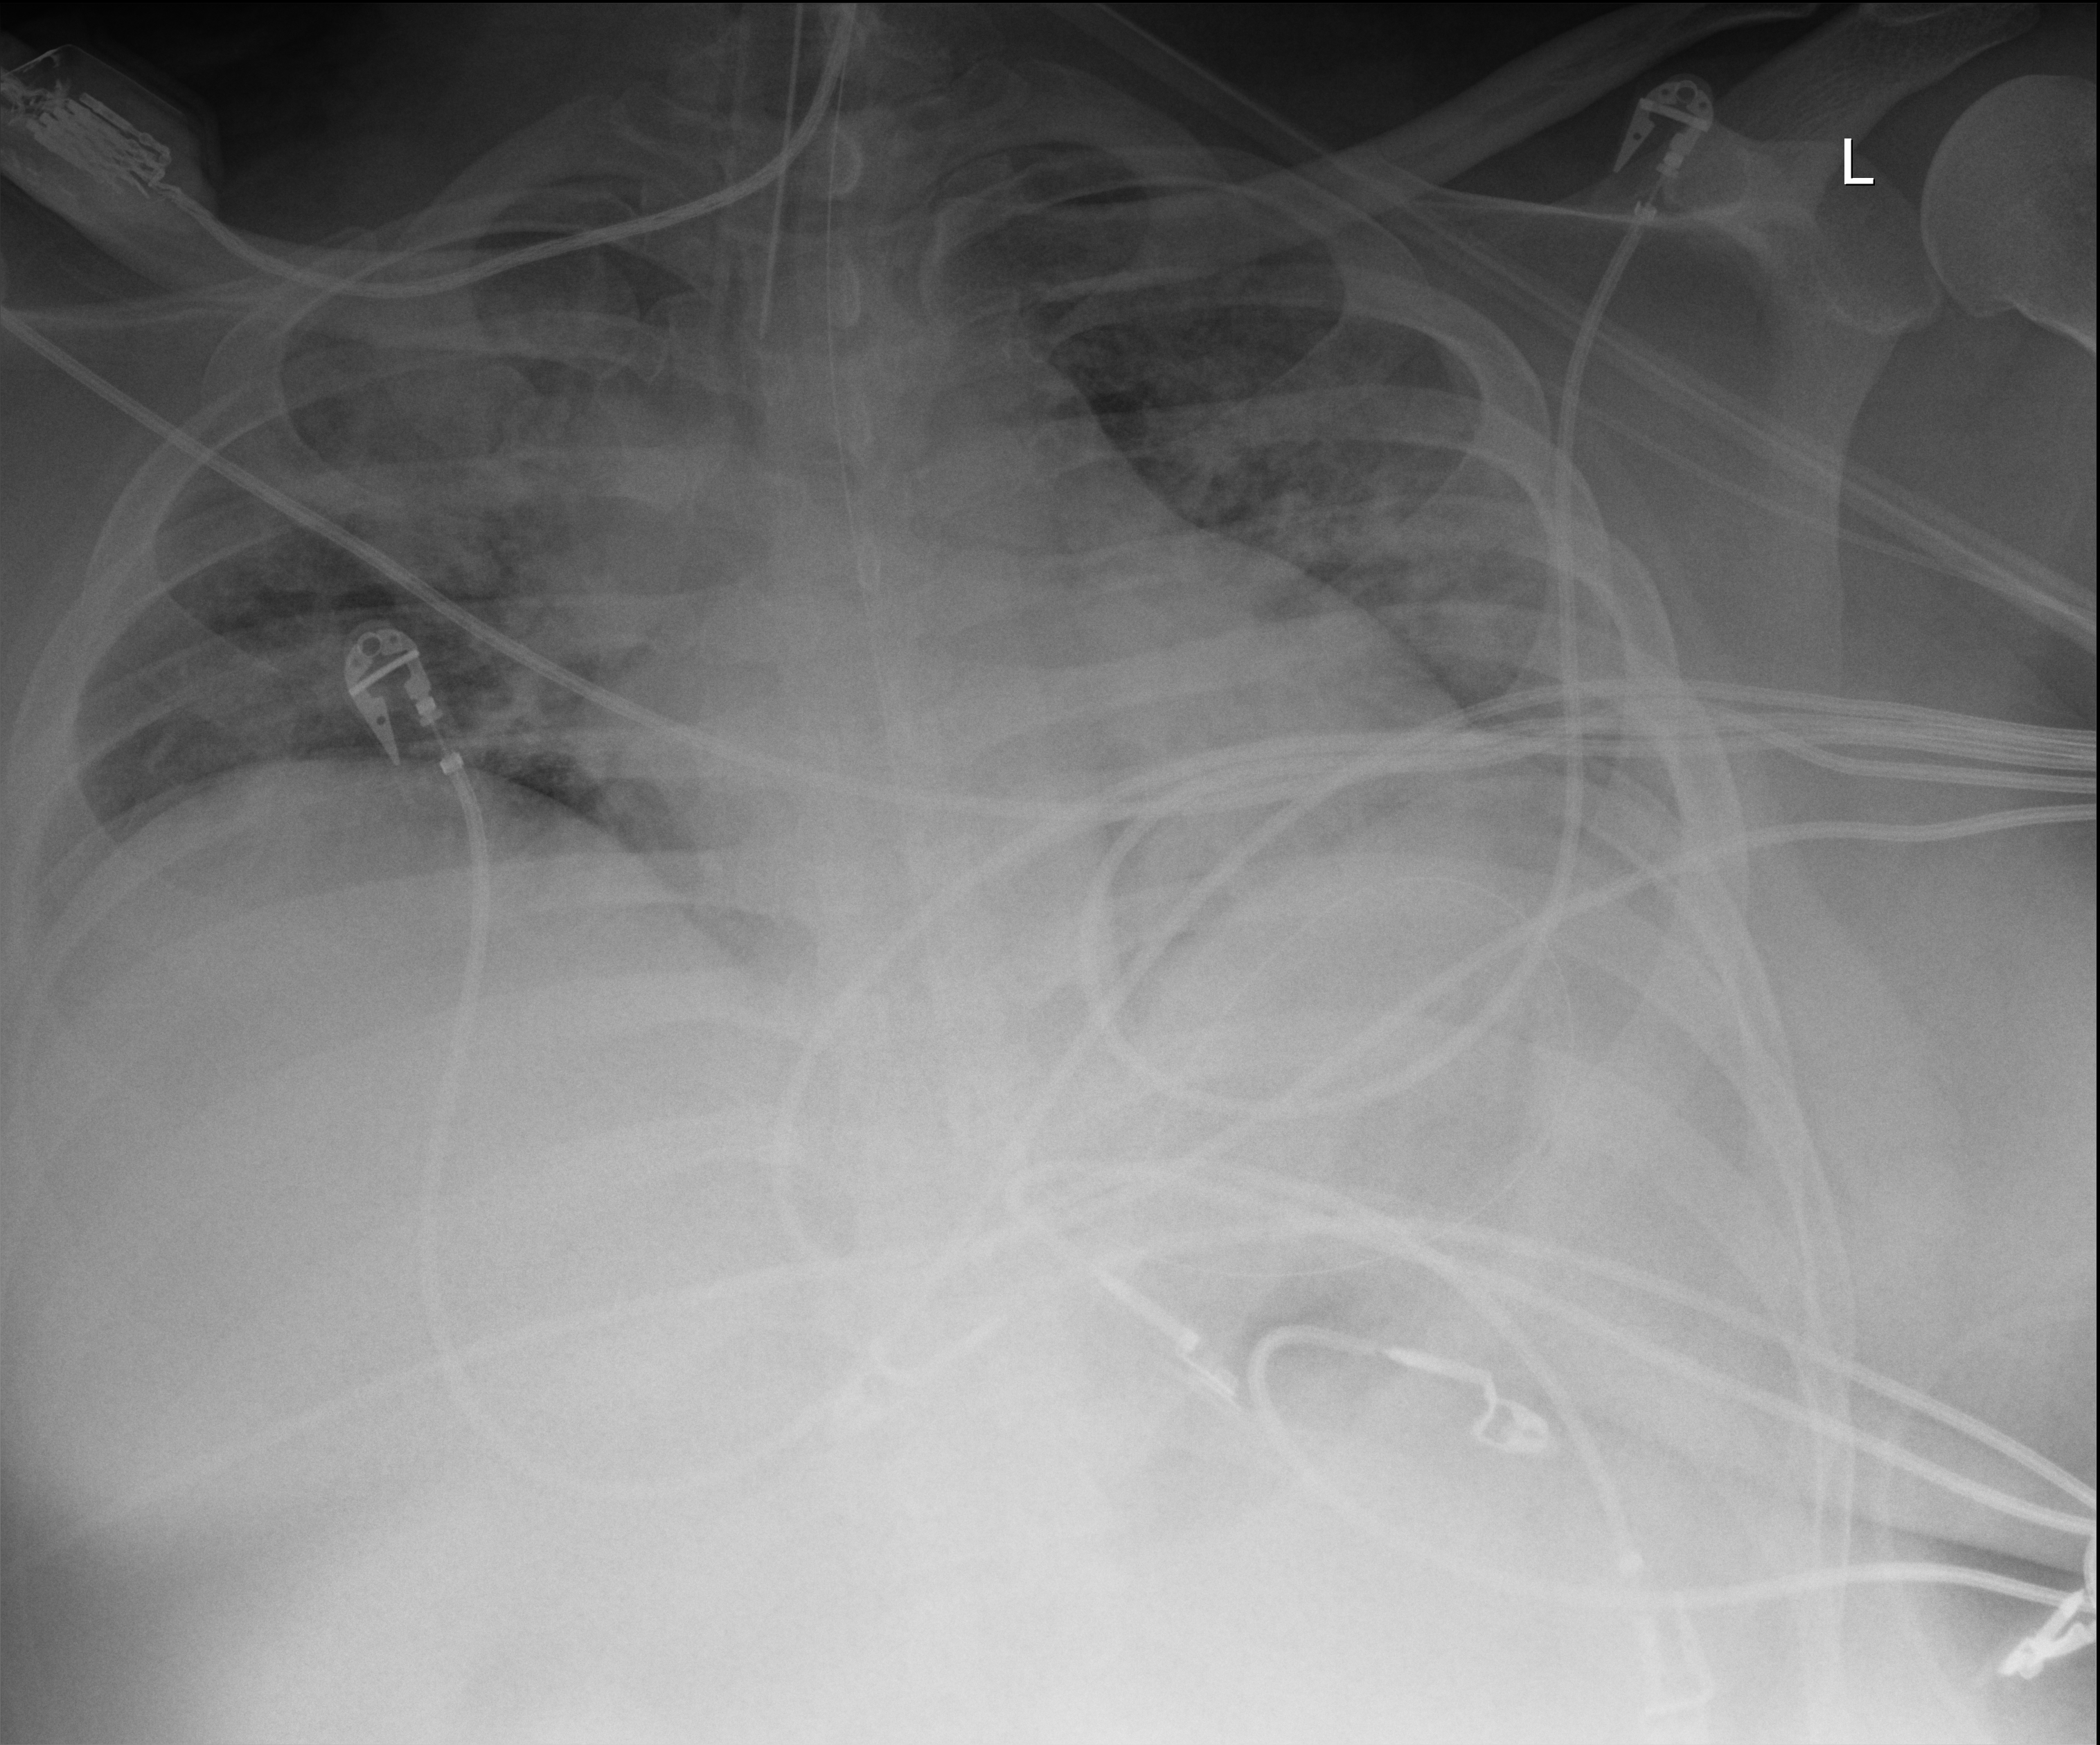
Chest X-ray (portable), anteroposterior (AP) projection. Patient hospitalised with COVID-19; male, aged 18–59 years.
Admission-level facts for this patient (not findings on this image; timing relative to this image not recorded):
- admitted to intensive care during this hospital stay: yes
- mechanically ventilated during this hospital stay: yes